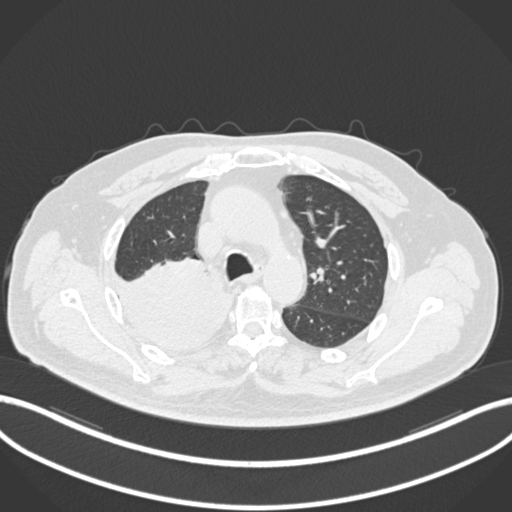
Chest CT, one axial slice. Slice 146 of 218 in the series (ordered by position). Reconstruction kernel B30f. 120 kVp. Lung window (W 1500 / L -600 HU). 512 × 512 image matrix, field of view 400 × 400 mm. Male patient, age 68 years. From the clinical record (not read from this slice): clinical TNM (as recorded): T2a N0 M0.
Structures marked on this image (bounding box drawn by a radiologist):
- lung tumour (recorded histology: adenocarcinoma): bounding box [x1, y1, x2, y2] px = [111, 258, 234, 357]